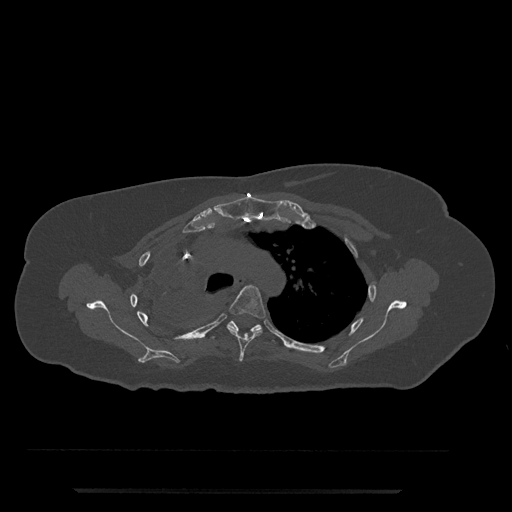
CT including the spine, one axial slice. Slice 574 of 797 in the series (ordered by position). Reconstruction kernel Br40s/3. 120 kVp. Bone window (W 1800 / L 400 HU). 0.5 mm slice thickness. 512 × 512 image matrix. Patient: female, 51 years. Case-level facts recorded for this patient, not image findings: primary cancer: neuro.
Structures marked on this image (semi-automatic segmentation, software-assisted and operator-edited):
- T4 vertebra: box from (x=211, y=285) to (x=266, y=362) px
- T5 vertebra: (x=211, y=321)–(x=278, y=342)